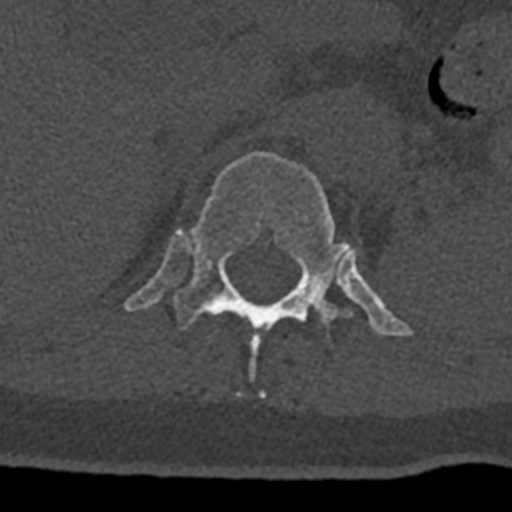
CT including the spine, one axial slice; slice 496 of 797 in the series (ordered by position); bone window (W 1800 / L 400 HU); 512 × 512 image matrix, field of view 160 × 160 mm. Male patient, age 74 years. From the clinical record (not read from this slice): primary cancer: renal.
Outlined on this slice (semi-automatic segmentation, software-assisted and operator-edited):
- T12 vertebra: bounding box <123,151,413,398> (left, top, right, bottom; pixels)